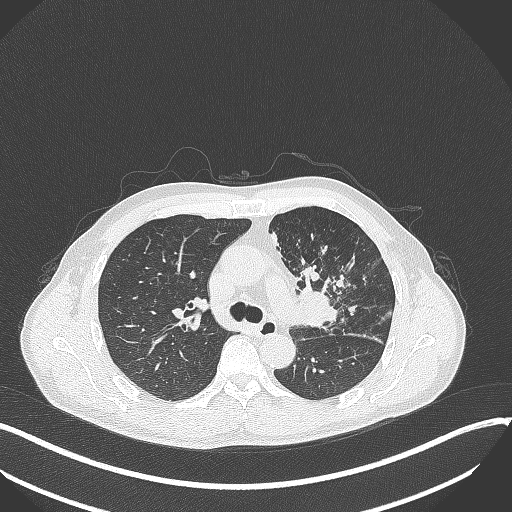
Chest CT, one axial slice; 120 kVp; lung window (W 1500 / L -600 HU); 1 mm slice thickness; 512 × 512 image matrix, field of view 400 × 400 mm. Patient: male, 56 years. From the clinical record (not read from this slice): clinical TNM (as recorded): T2a N0 M0.
Structures marked on this image (rectangle marked by the reading radiologist):
- lung tumour (recorded histology: squamous cell carcinoma): bounding box <290,279,343,330> (left, top, right, bottom; pixels)